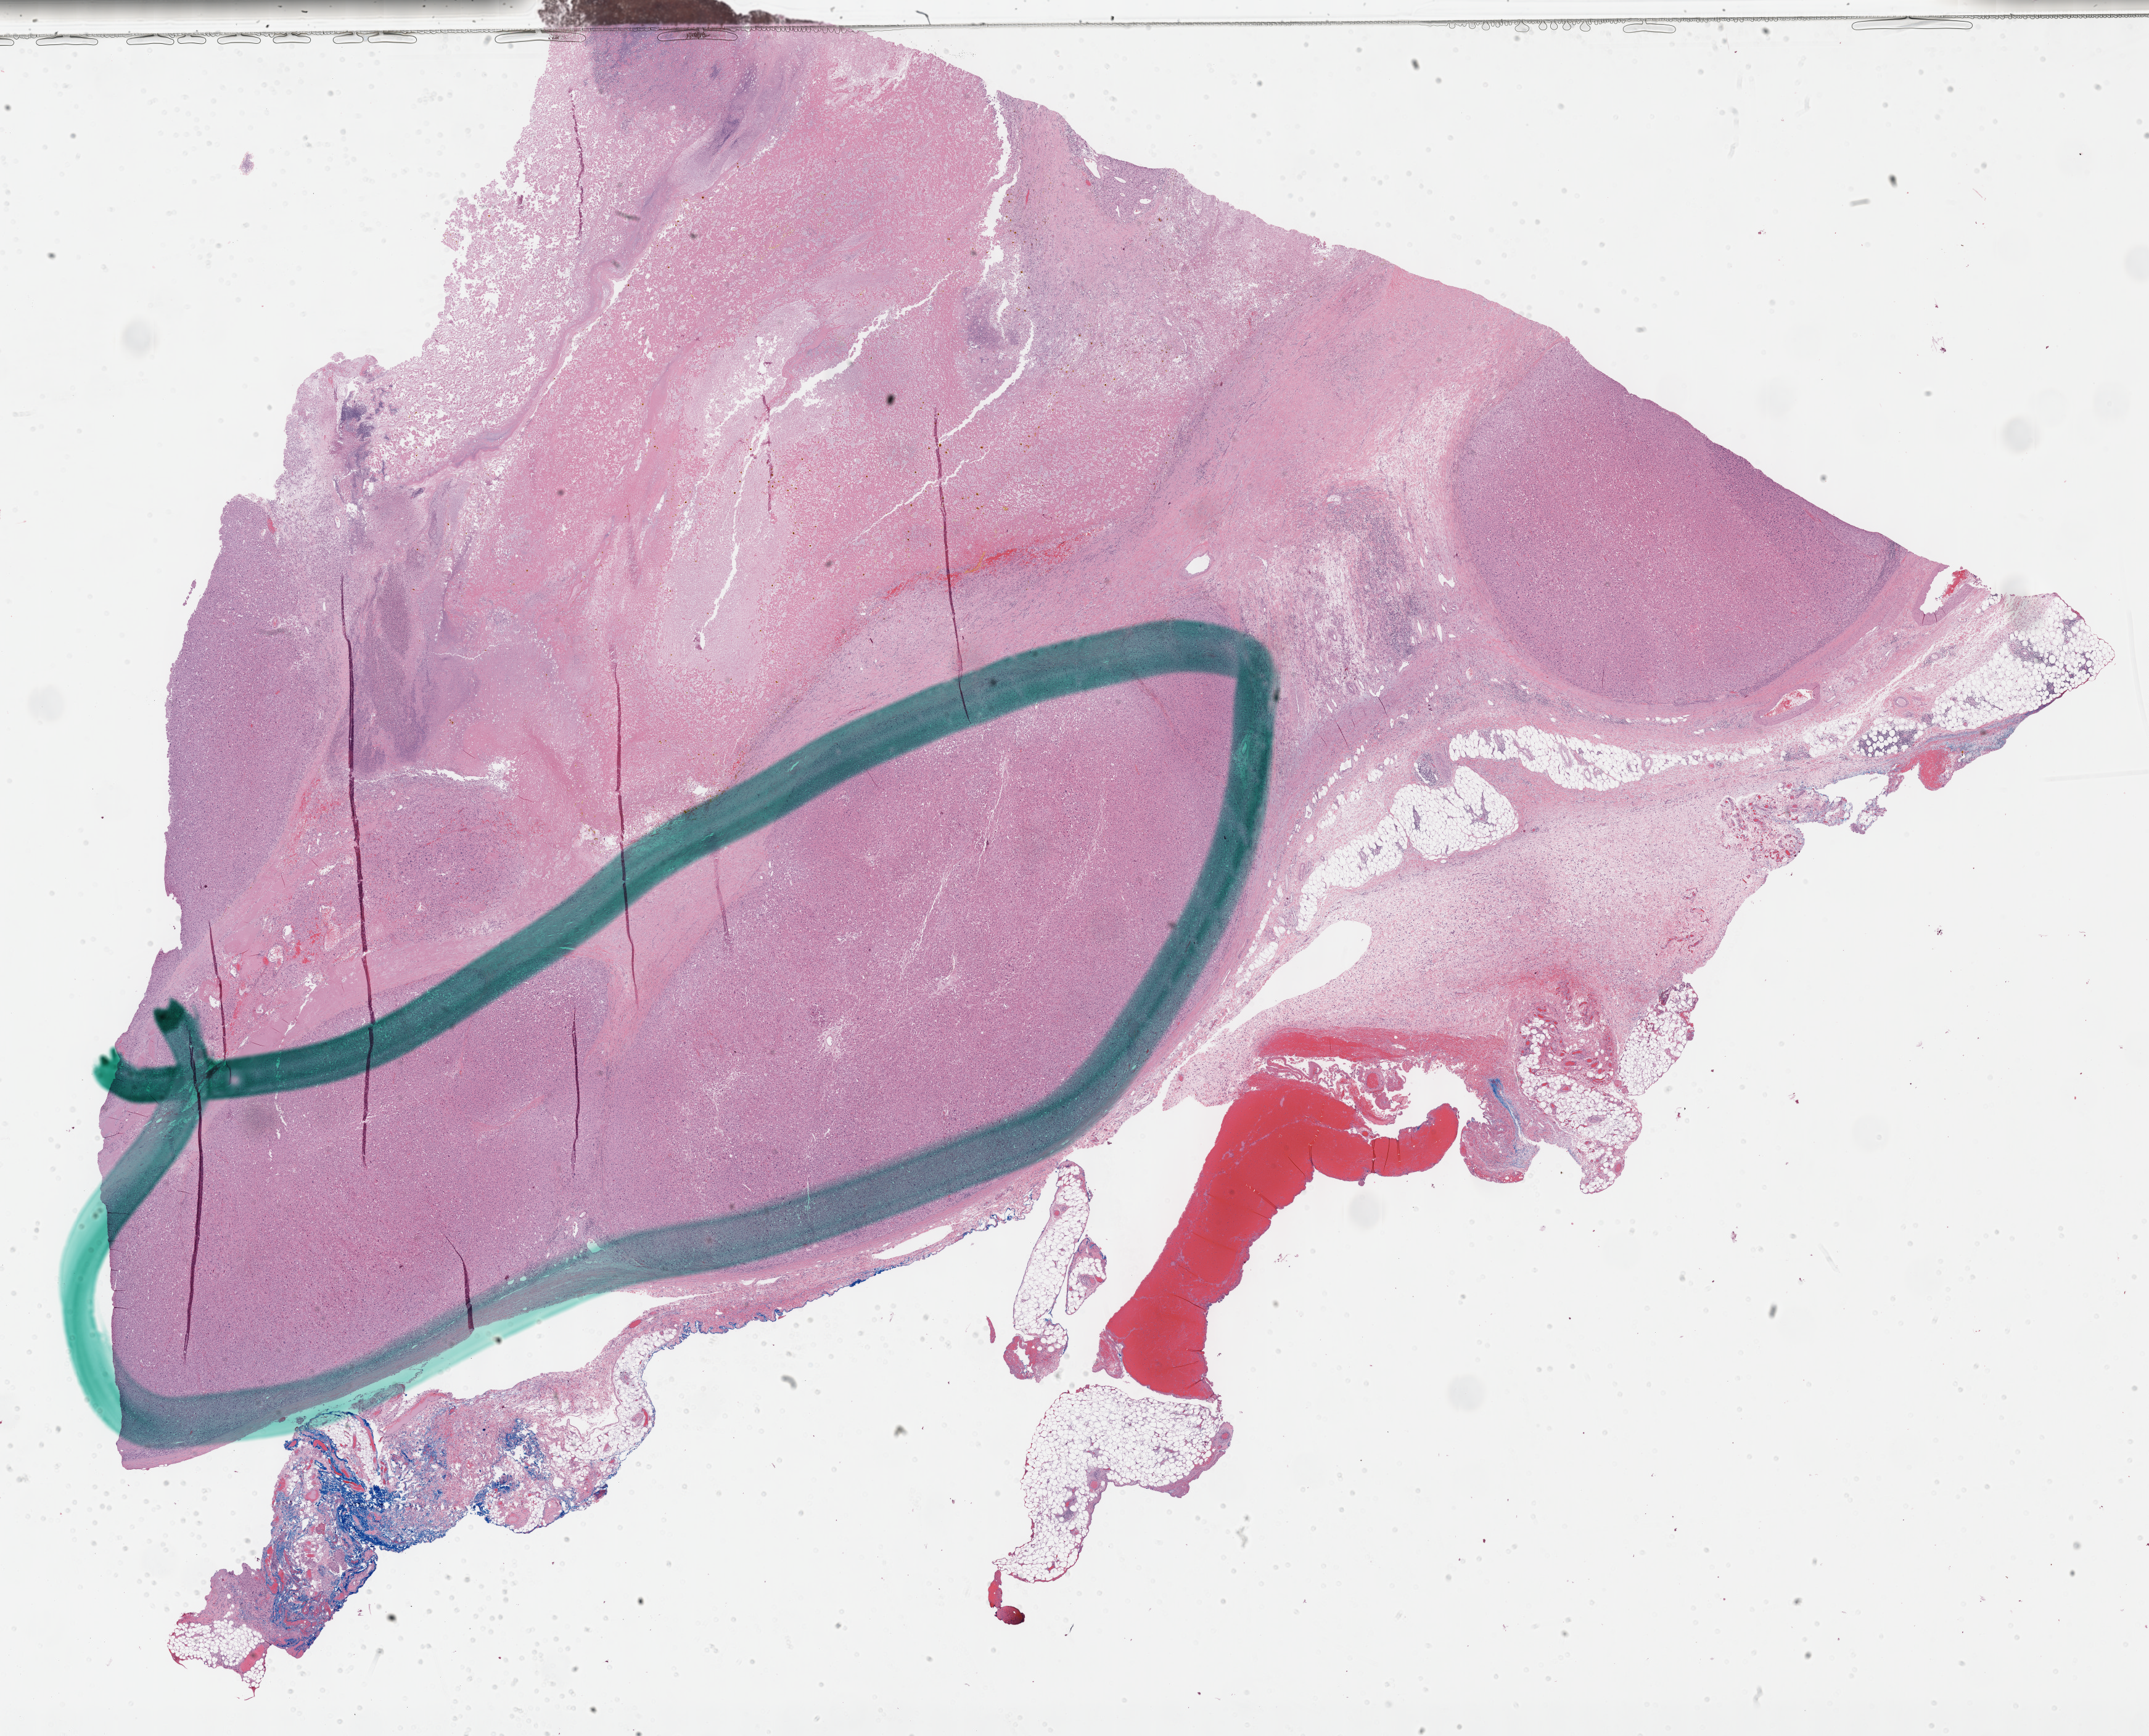
H&E whole-slide image, shown as a low-resolution overview of the whole scanned area (about 28.2 x 22.8 mm, slide scanned at 40x); formalin-fixed paraffin-embedded (FFPE) diagnostic section; primary tumour sample from the adrenal cortex. Female patient; age at initial diagnosis 65 years.
Histologic diagnosis: Adrenal cortical carcinoma (cortex of adrenal gland).